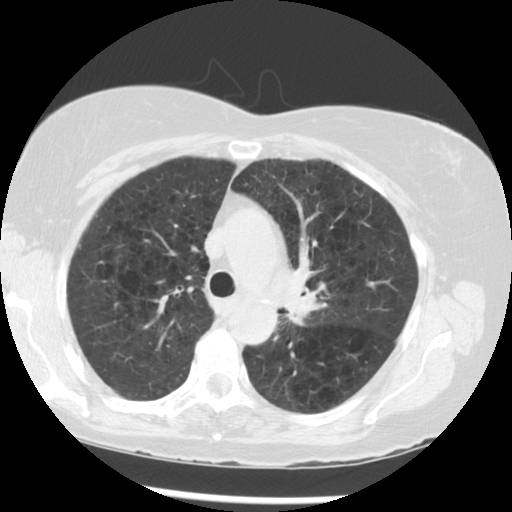
Low-dose screening chest CT, one axial slice. Slice 206 of 283 in the series (ordered by position). Reconstruction kernel STANDARD. 120 kVp. Lung window (W 1500 / L -600 HU). 512 × 512 image matrix, field of view 330 × 330 mm.
Annotated regions visible in this slice (outlined manually by an expert reader):
- lesion 1 (tumor, upper lobe of left lung): bounding box <288,301,320,323> (left, top, right, bottom; pixels)